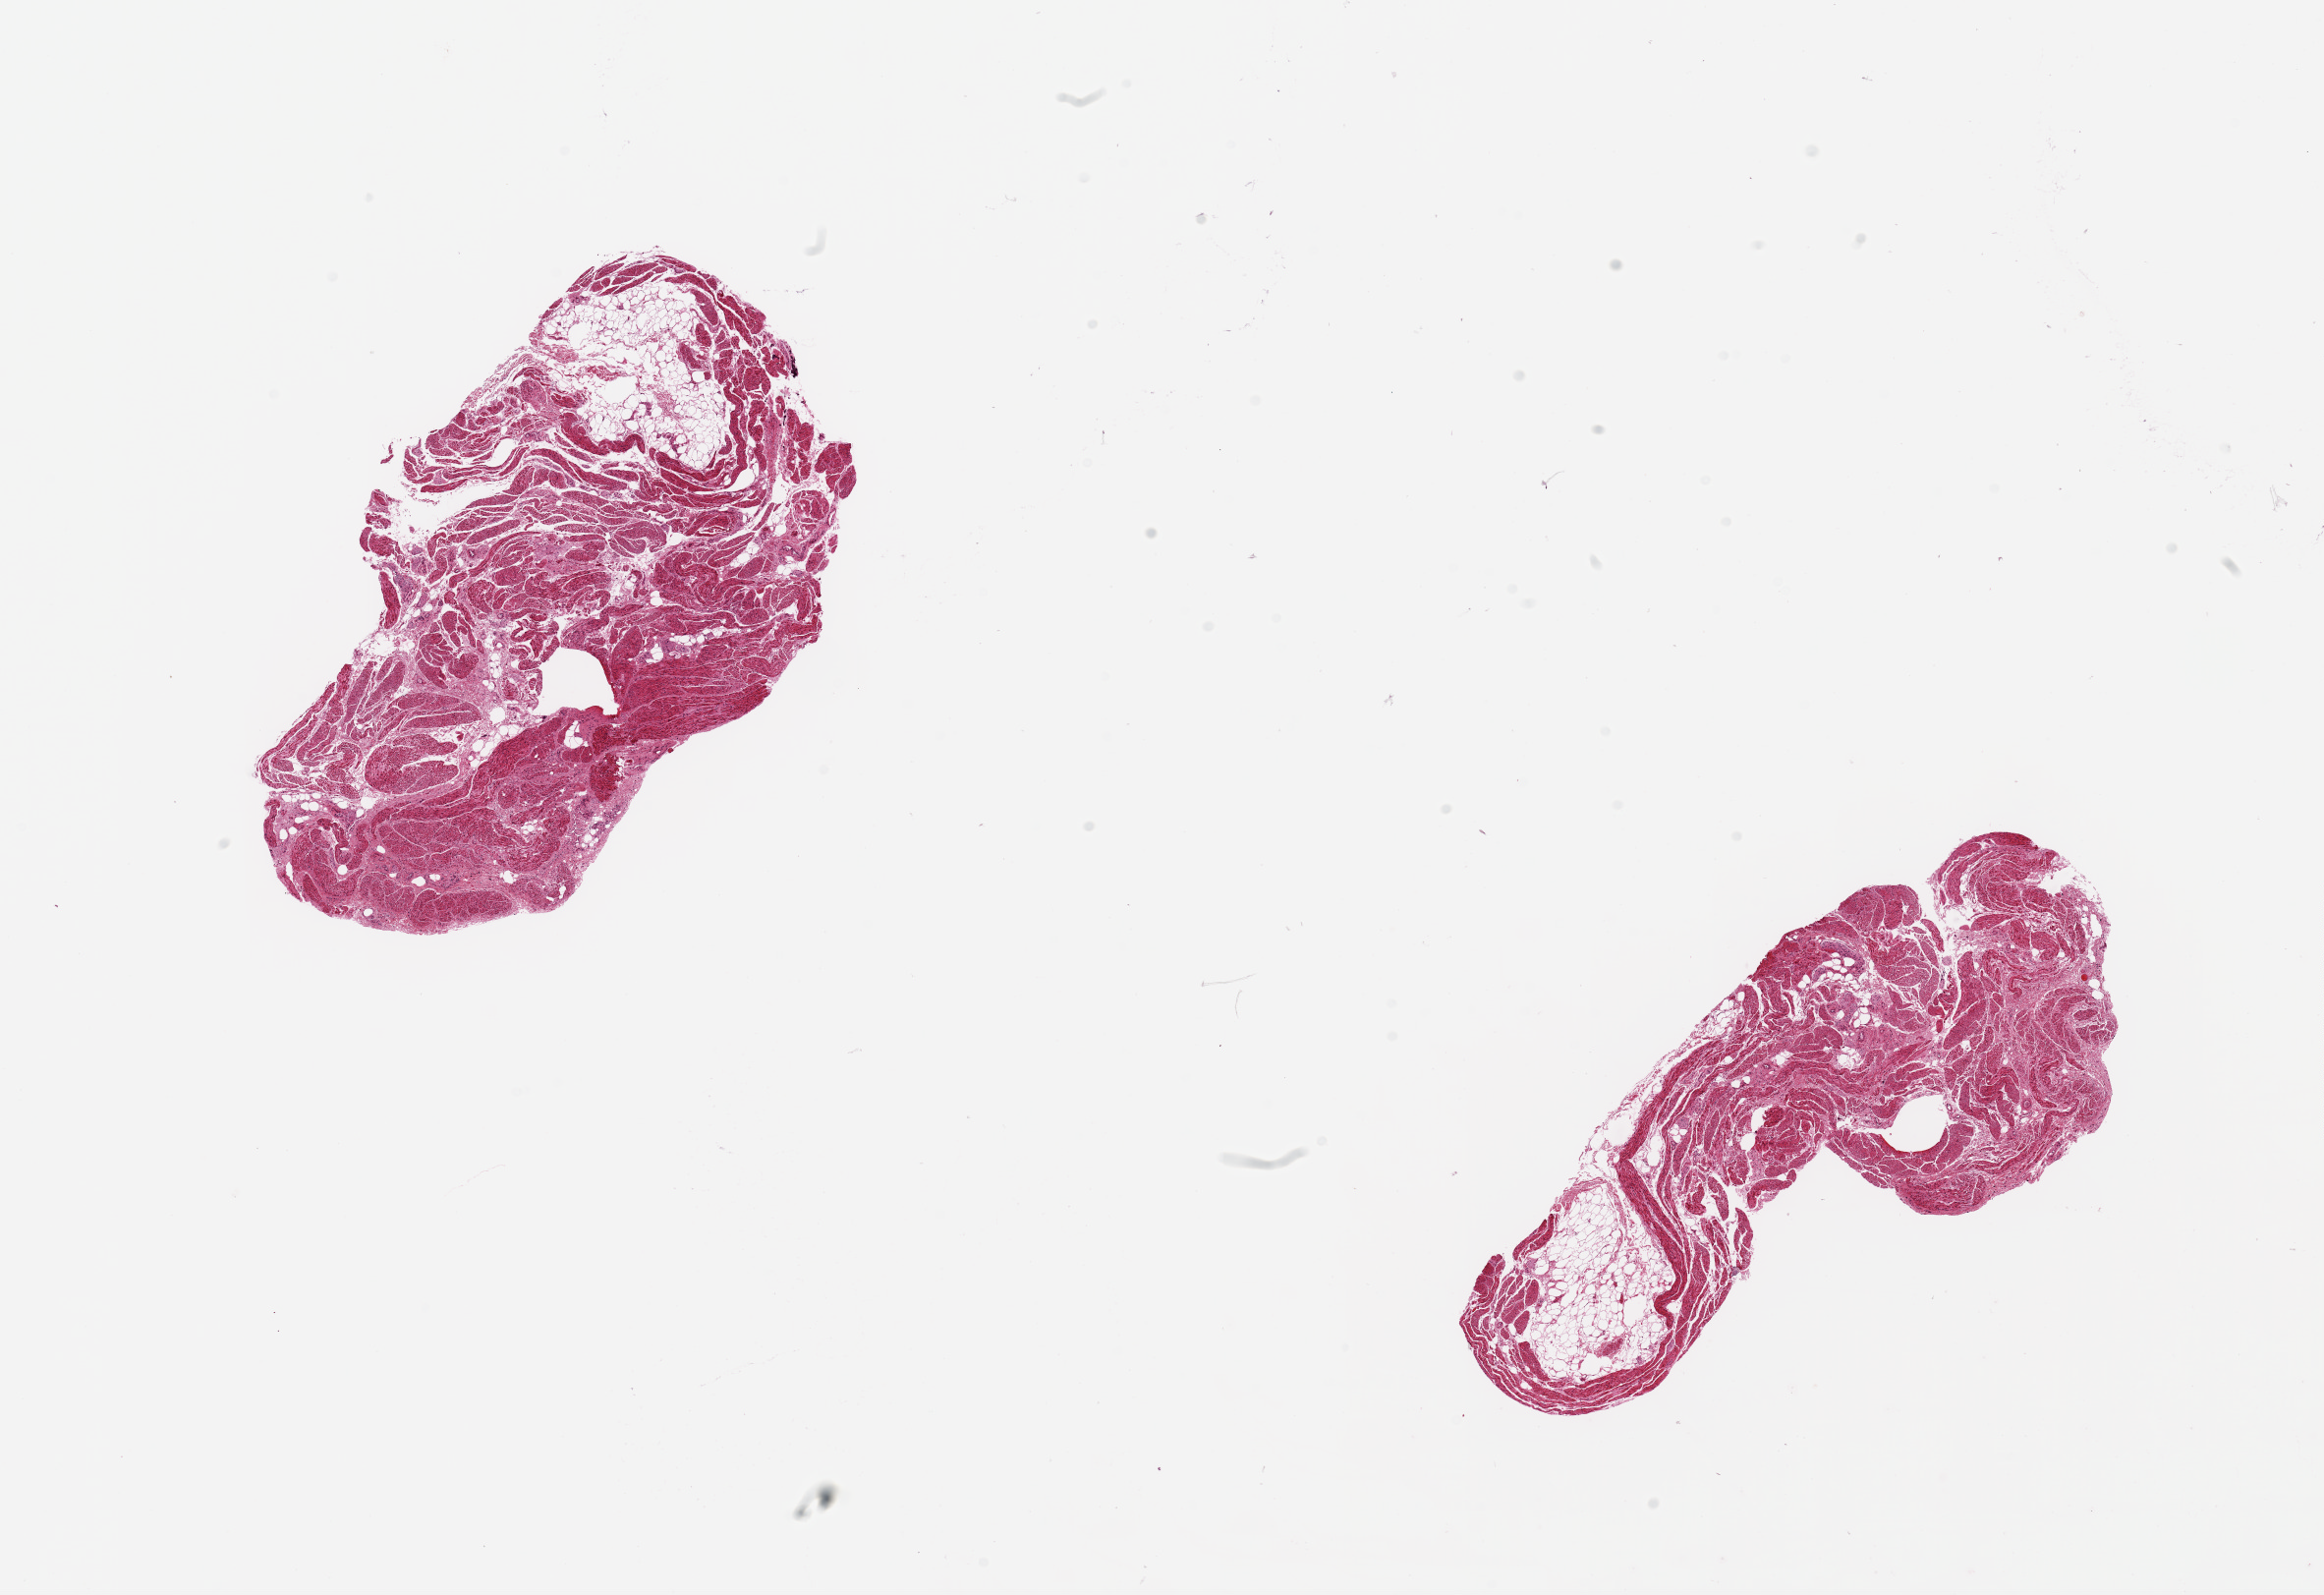
Digitized haematoxylin and eosin-stained section, low-resolution overview of the scanned area, about 18.7 x 12.8 mm, PAXgene-fixed paraffin-embedded (PFPE) section, target tissue: urinary bladder, tissue donor sample.
Pathologist's review note for this sample: Two 6x3.5mm pieces. Foci of central fat; focally poorly fixed. Mucosa completely sloughed.